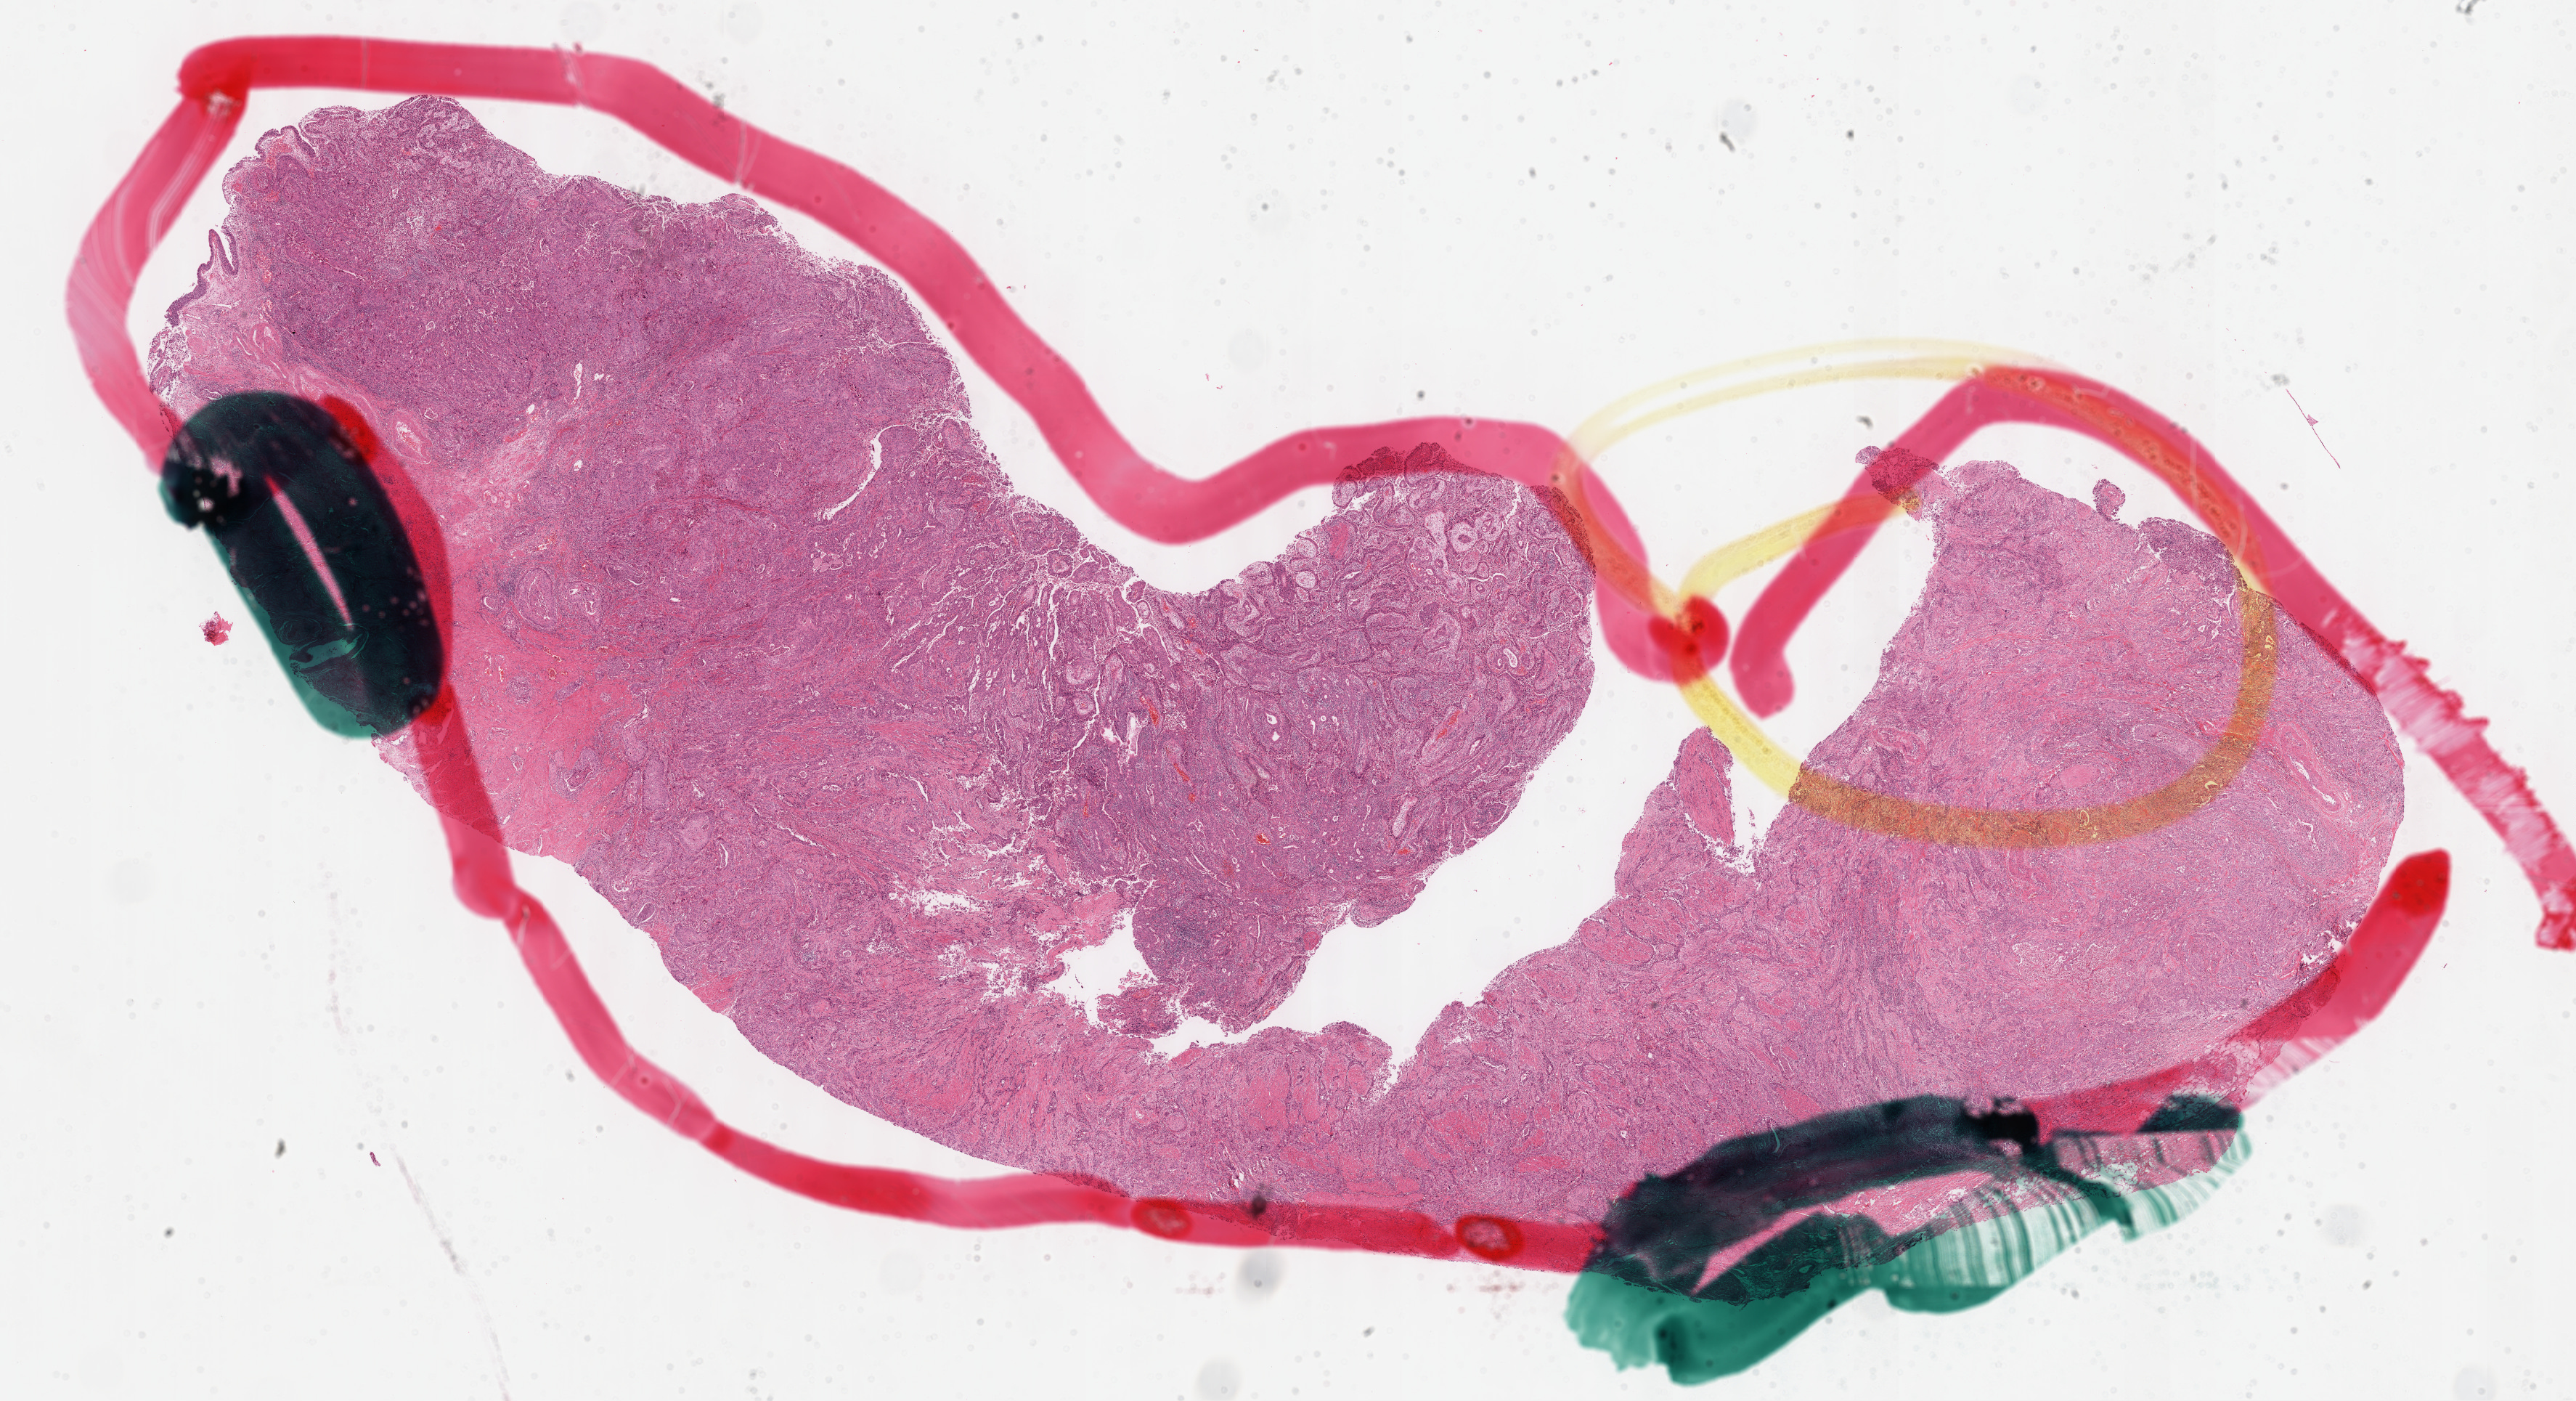
Whole-slide histology image, H&E-stained — whole scanned area (about 28.7 x 15.6 mm, acquisition: 40x scan) shown as a low-resolution overview; formalin-fixed paraffin-embedded (FFPE) diagnostic section; sample: primary tumour, bladder. Male patient; age at initial diagnosis 73 years. Histologic grade: high grade.
* histologic diagnosis: Transitional cell carcinoma
* AJCC pathologic stage: II